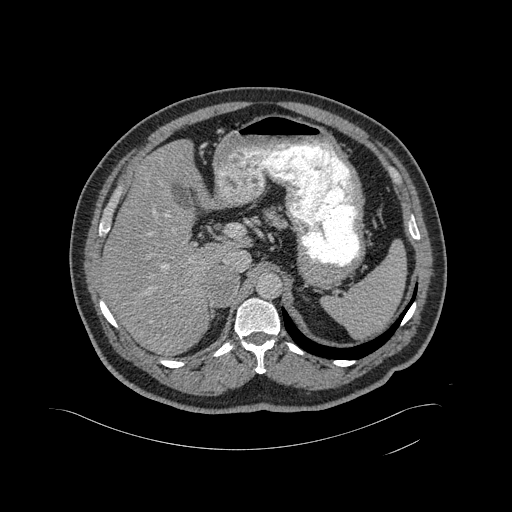
Contrast-enhanced abdominal CT, one axial slice. Position 329 of 433 along the scan axis. 120 kVp. Intravenous contrast given. Soft-tissue window (W 400 / L 40 HU). 512 × 512 image matrix. Male patient, age 56 years. Case-level facts recorded for this patient, not image findings: diagnosis: adrenocortical carcinoma; tumour side: right adrenal; tumour size at pathology: 11.6 cm; Ki-67 index: 50 %; stage (as recorded): 3.
Structures marked on this image (semi-automatically segmented with operator editing):
- mass: bounding box <207,267,238,306> (left, top, right, bottom; pixels)